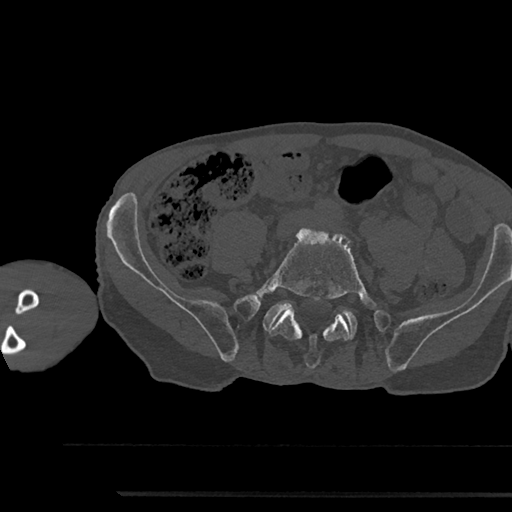
CT including the spine, one axial slice. Slice 338 of 797 in the series (ordered by position). 120 kVp. Bone window (W 1800 / L 400 HU). 0.5 mm slice thickness. 512 × 512 image matrix, field of view 367 × 367 mm. Patient: male, 79 years. Case-level facts recorded for this patient, not image findings: primary cancer: prostate.
Annotated regions visible in this slice (semi-automatically segmented with operator editing):
- L5 vertebra: box from (x=254, y=227) to (x=377, y=369) px